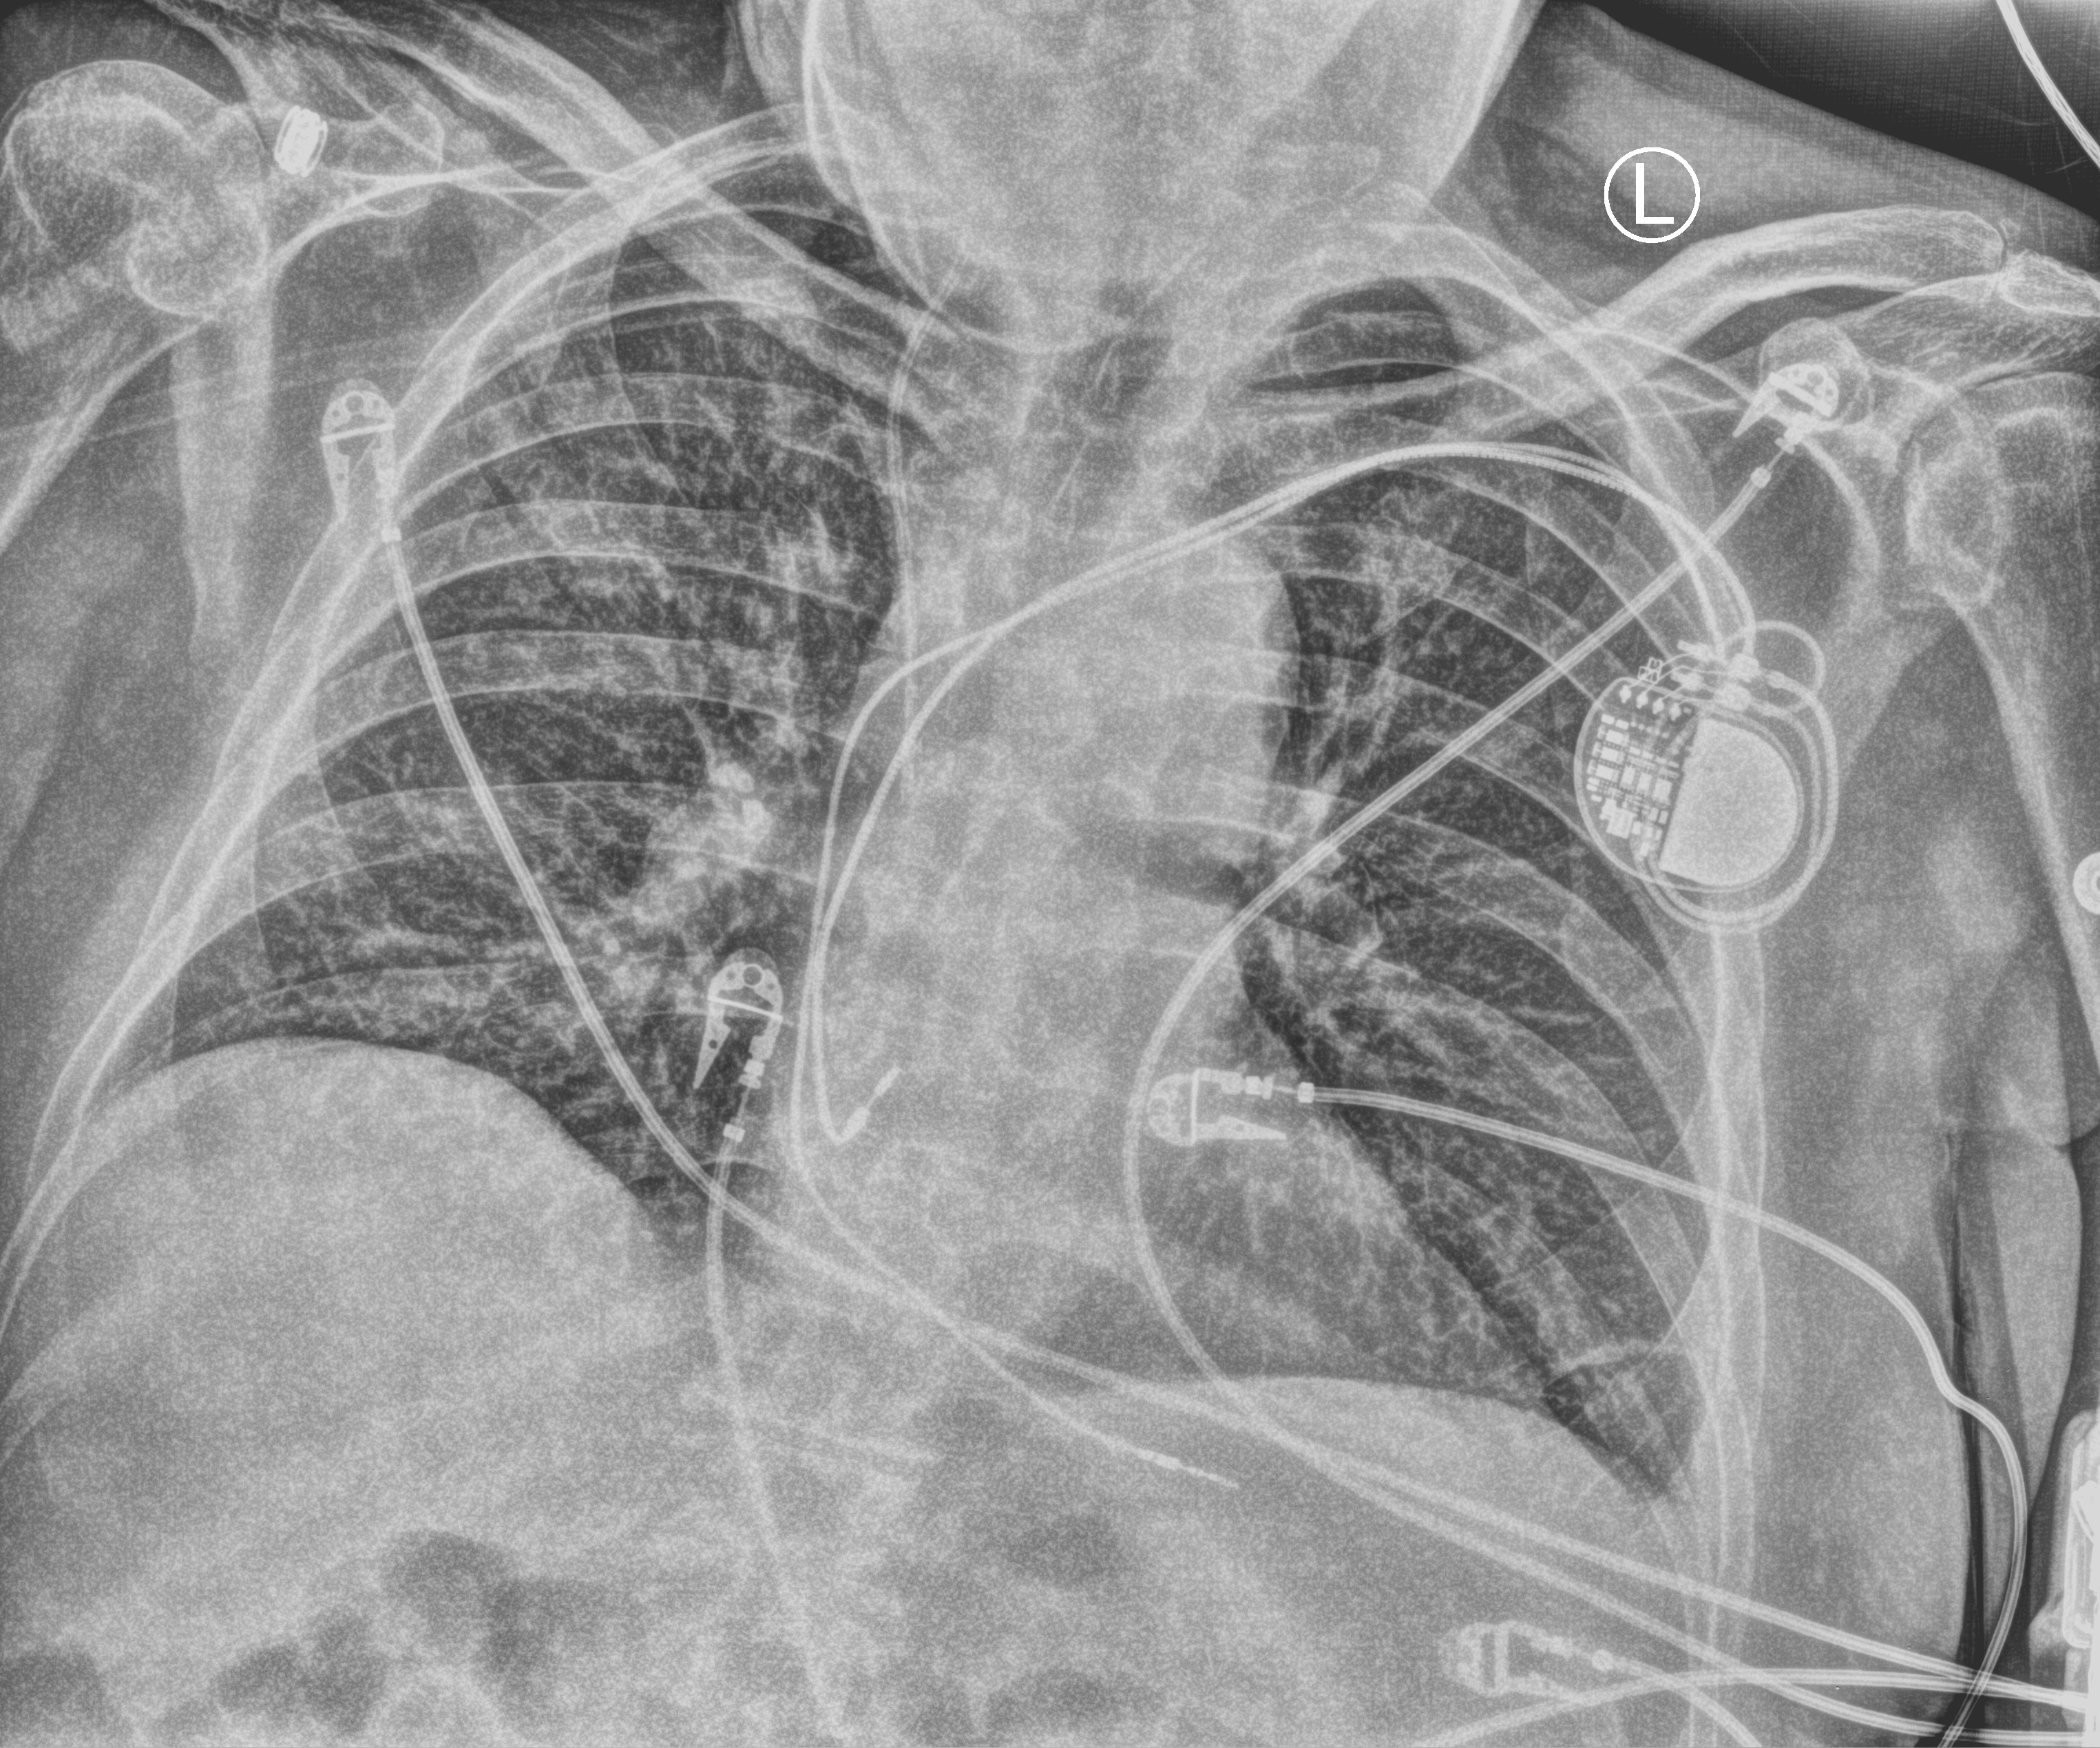
Portable chest radiograph, anteroposterior (AP) projection. Male patient hospitalised with COVID-19, age 60–74 years.
From the hospital-stay record, not from the radiograph (when in the stay this image was taken is not recorded):
- mechanically ventilated during this hospital stay: no
- length of hospital stay: 6 days
- COPD (admission record): yes